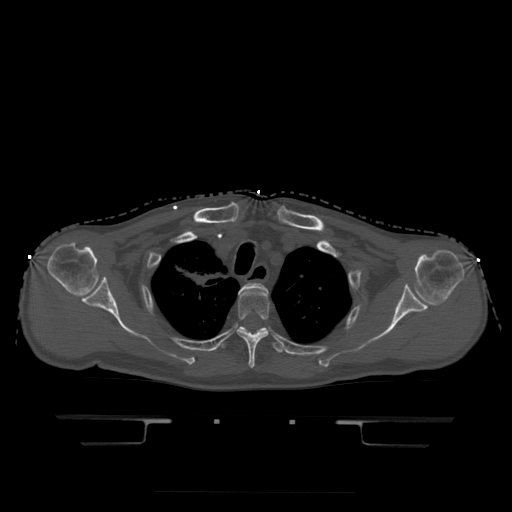
CT including the spine, one axial slice. Slice 368 of 522 in the series (ordered by position). Bone window (W 1800 / L 400 HU). 1.25 mm slice thickness. 512 × 512 image matrix. Patient age 68 years. From the clinical record (not read from this slice): primary cancer: urothelial.
Annotated regions visible in this slice (semi-automatic segmentation, software-assisted and operator-edited):
- T2 vertebra: box from (x=241, y=284) to (x=266, y=292) px
- T3 vertebra: (x=237, y=287)–(x=269, y=369)
- T4 vertebra: (x=219, y=326)–(x=283, y=354)